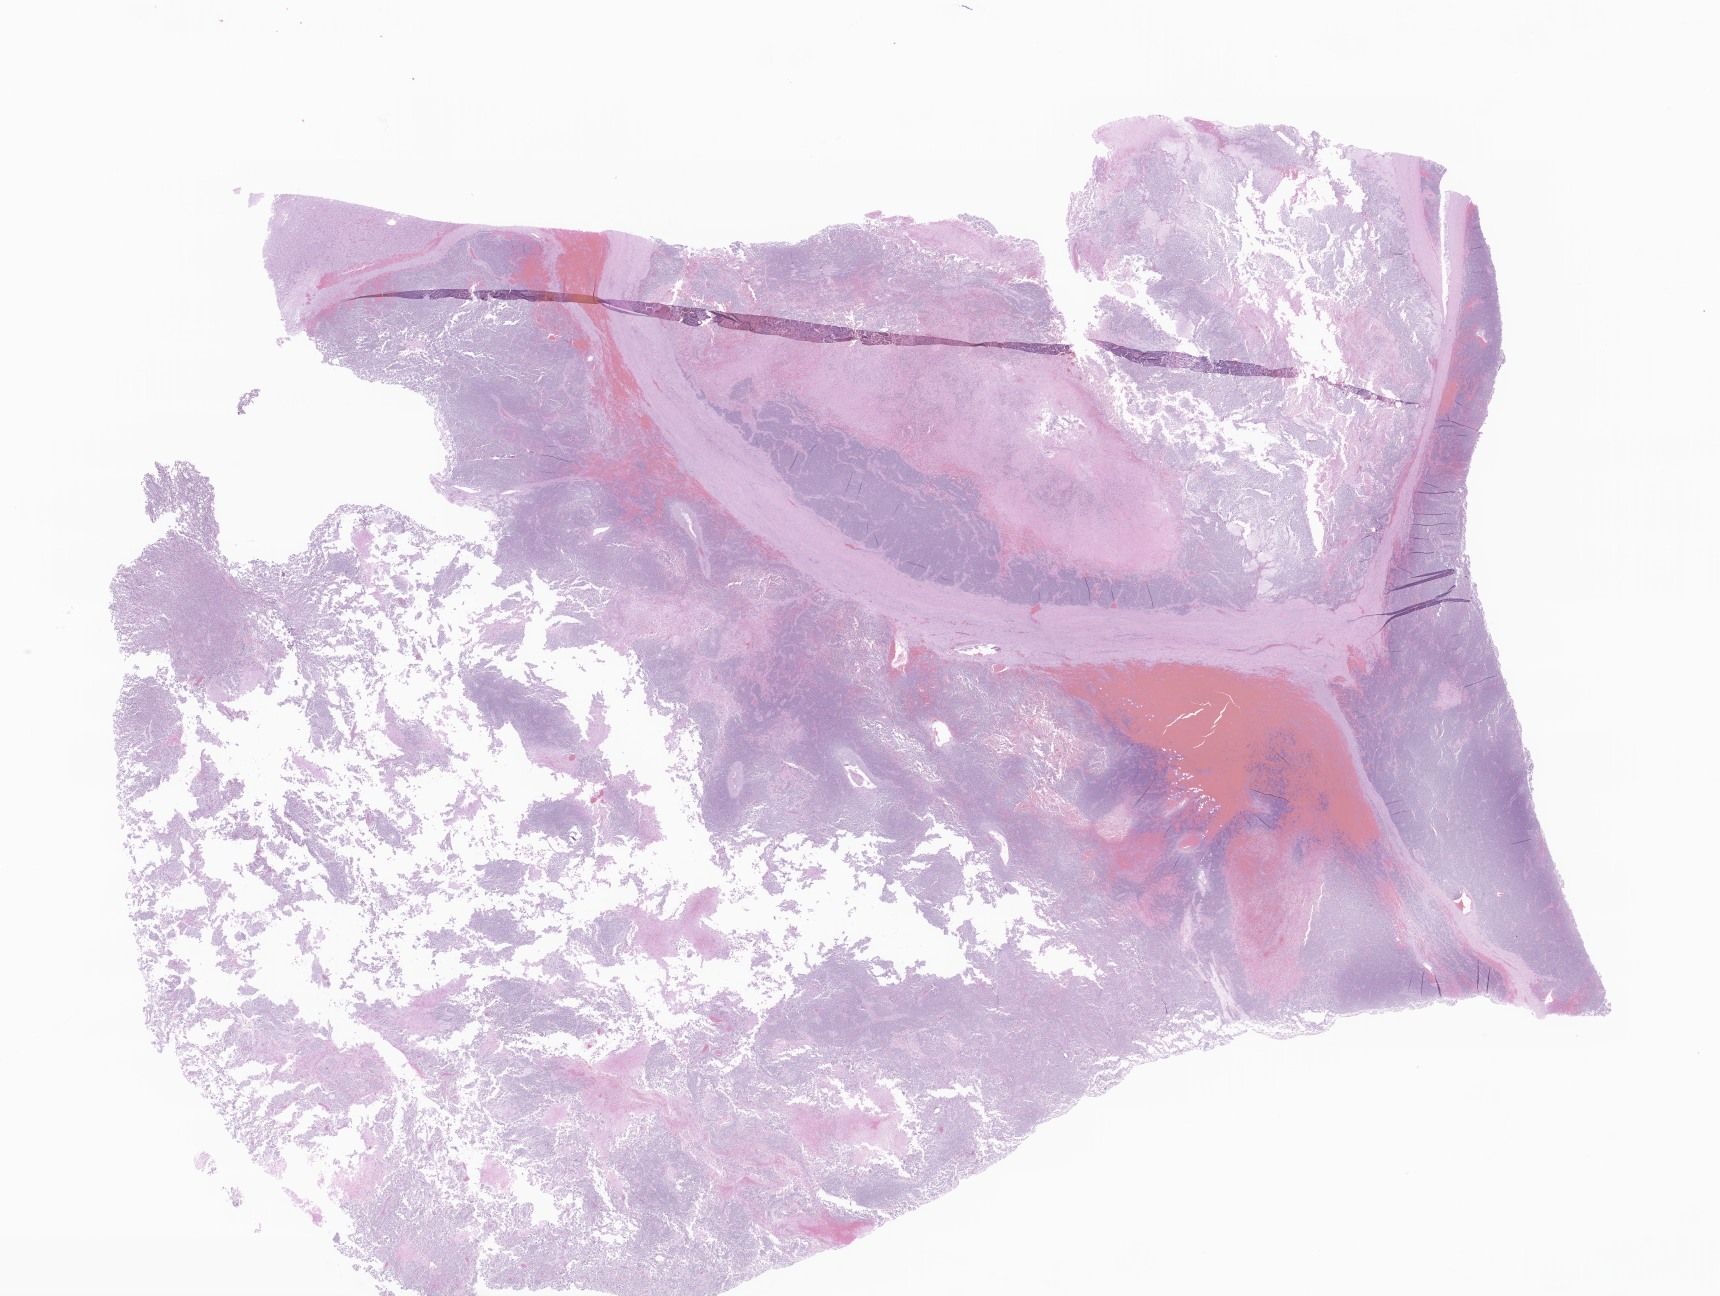
Whole-slide image, haematoxylin and eosin stain of tumor tissue from the kidney — whole scanned area (about 29.0 x 21.9 mm) shown as a low-resolution overview. FFPE section. Male patient, age 36 months (3 years).
Diagnosis (ICD-O-3 morphology term): Neuroblastoma, NOS.